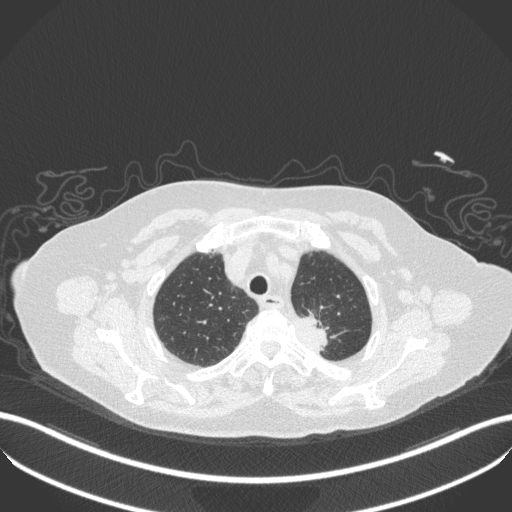
Chest CT, one axial slice; slice 285 of 353 in the series (ordered by position); lung window (W 1500 / L -600 HU); 1 mm slice thickness; 512 × 512 image matrix. Female patient, age 81 years. Case-level facts recorded for this patient, not image findings: clinical TNM (as recorded): T2a N0 M0.
Outlined on this slice (bounding box drawn by a radiologist):
- lung tumour (recorded histology: adenocarcinoma): bounding box (x1, y1, x2, y2) in pixels: (280, 309, 328, 356)